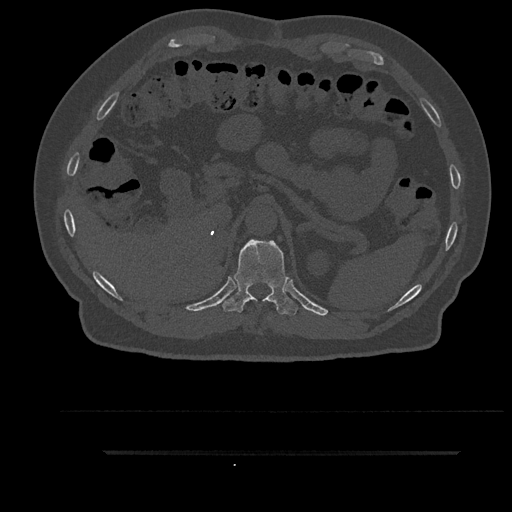
CT including the spine, one axial slice; slice 314 of 797 in the series (ordered by position); bone window (W 1800 / L 400 HU); 0.5 mm slice thickness; 512 × 512 image matrix, field of view 432 × 432 mm. Male patient, age 63 years. From the clinical record (not read from this slice): primary cancer: renal.
Structures marked on this image (semi-automatic segmentation, software-assisted and operator-edited):
- T11 vertebra: bounding box (x1, y1, x2, y2) in pixels: (223, 239, 298, 316)